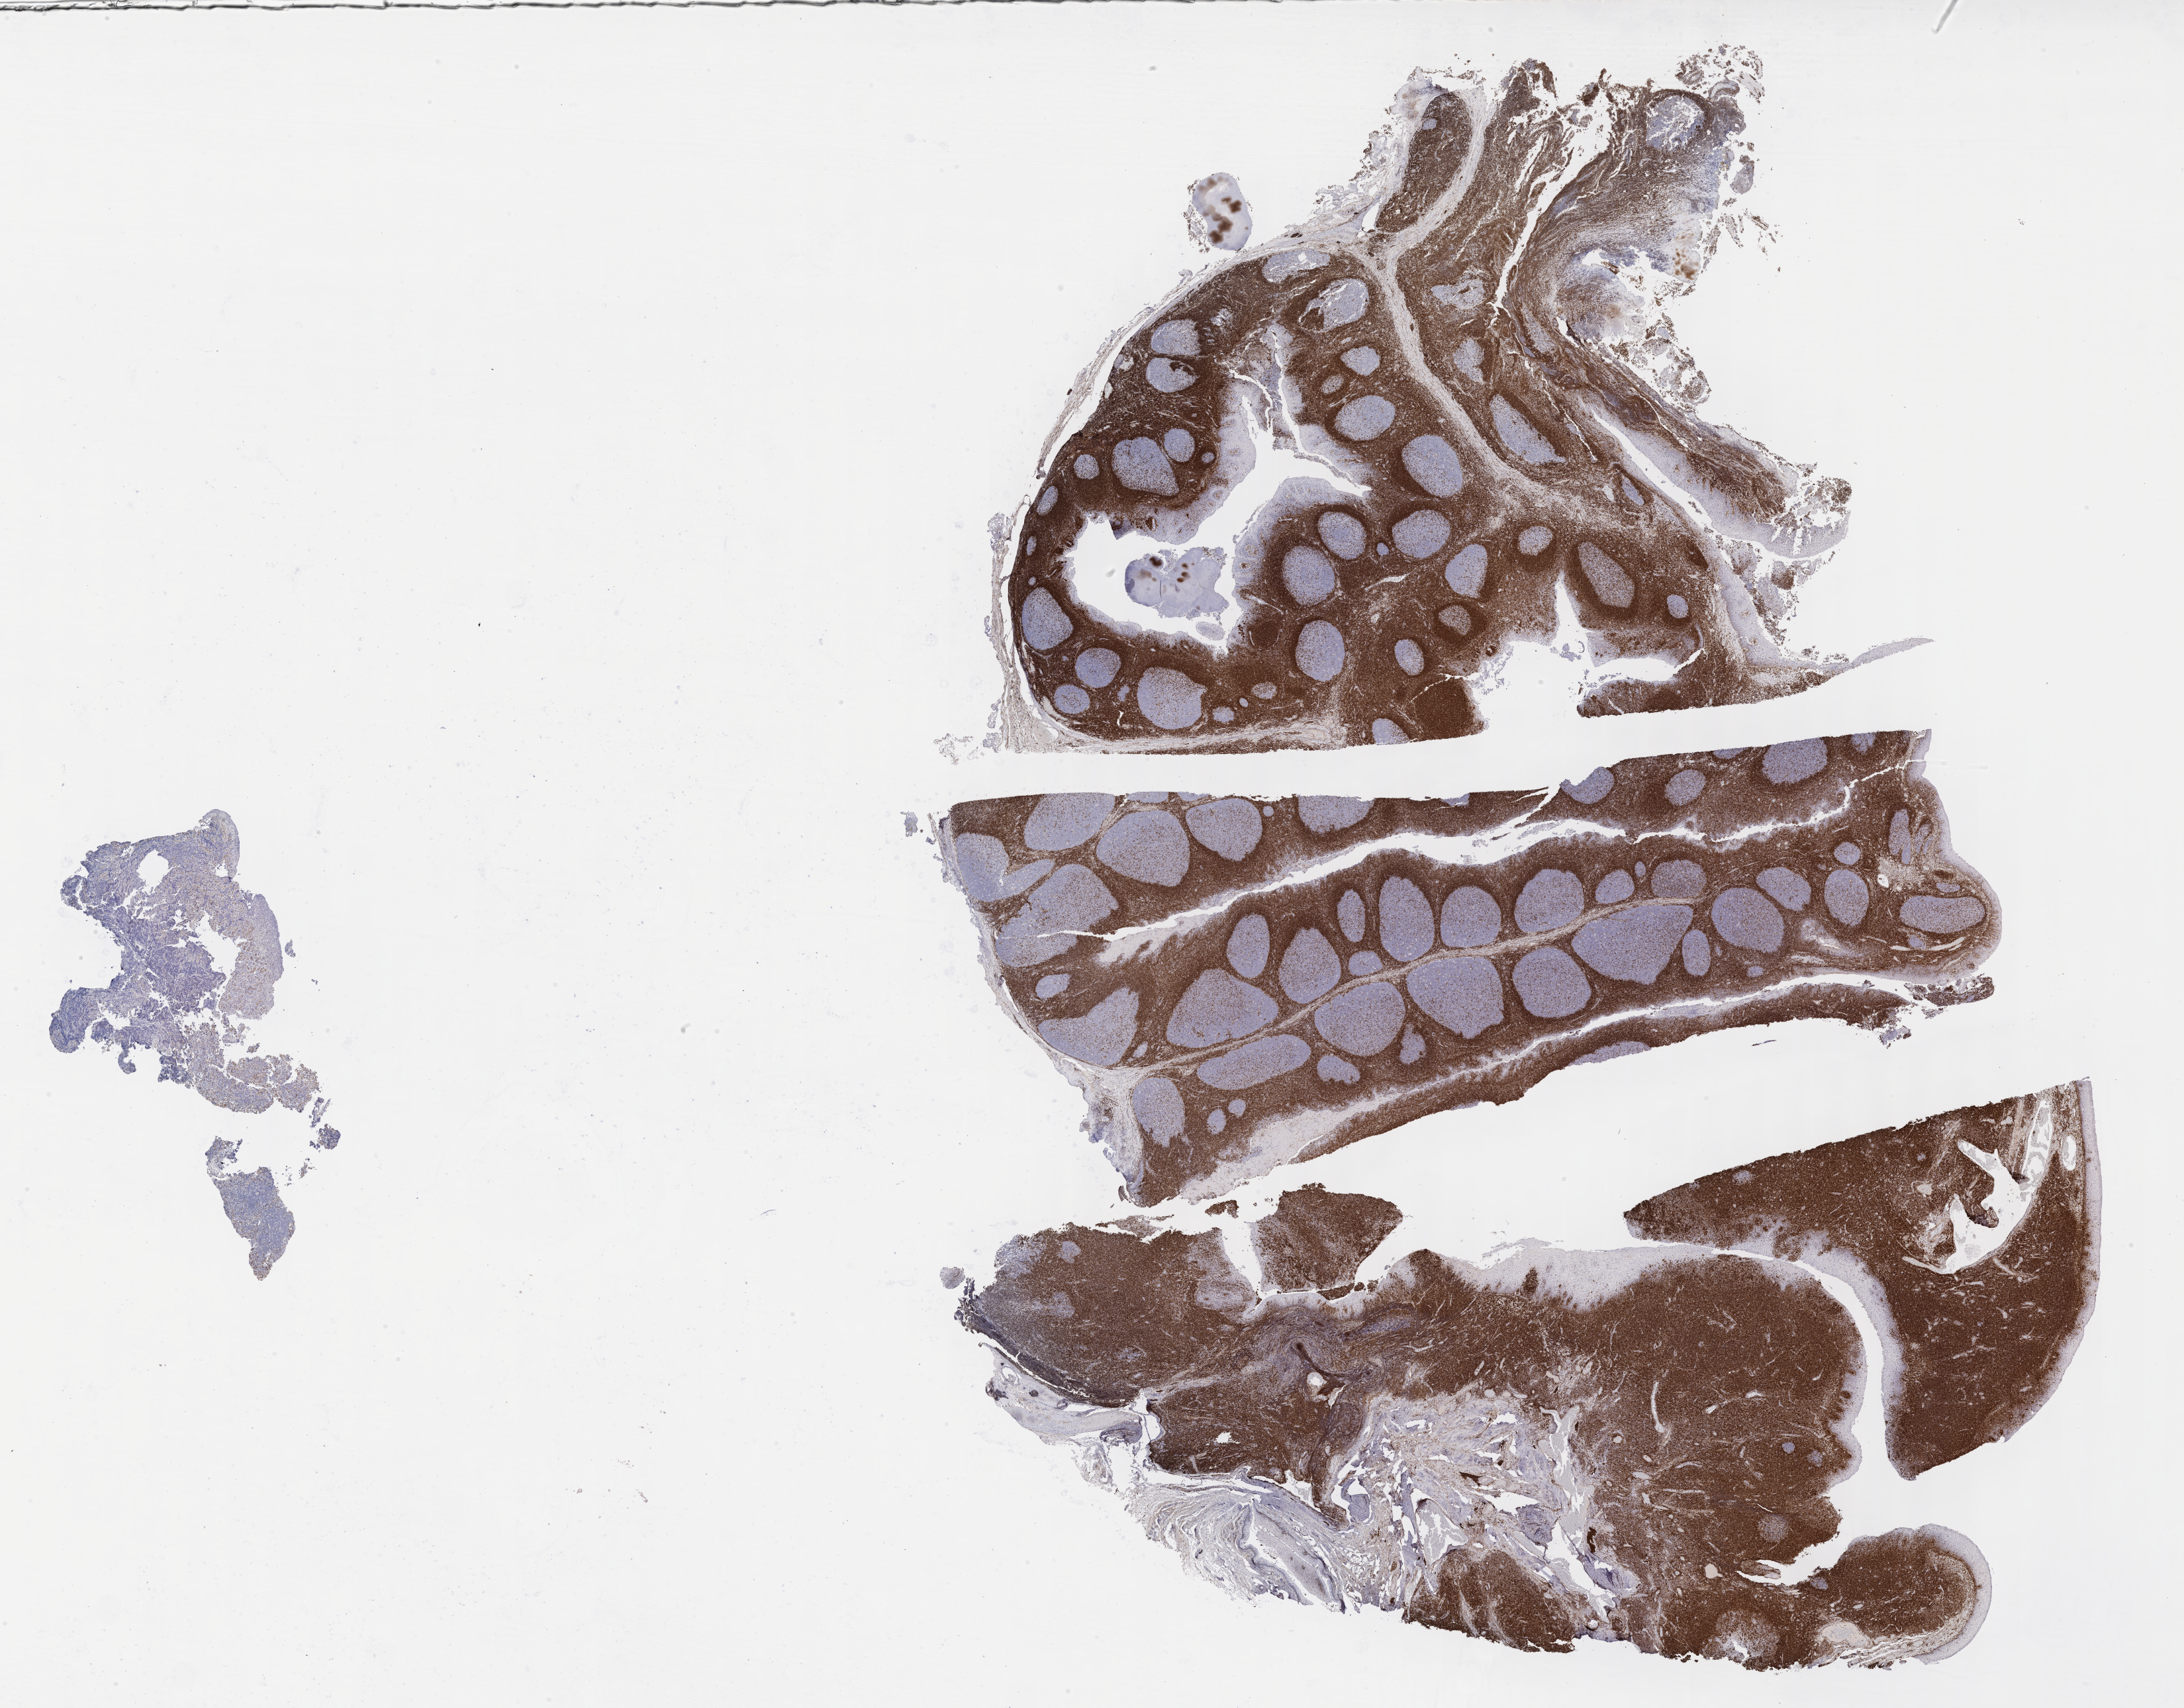
IHC for BCL2, whole-slide image — shown as a low-resolution overview of the whole scanned area (about 26.7 x 20.9 mm); specimen: tumor tissue; site: gum of mandible. Patient male; aged 10.
Histologic diagnosis: Burkitt lymphoma, NOS.